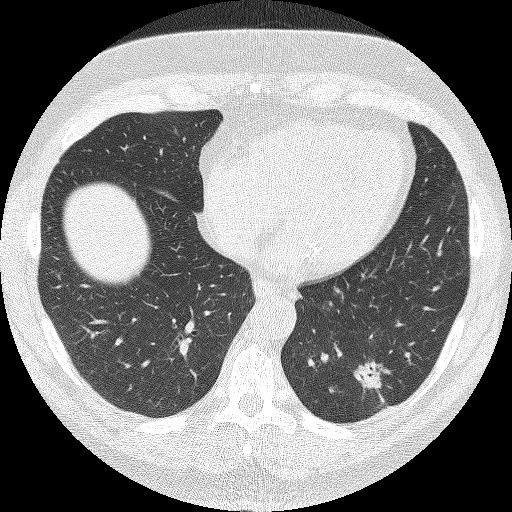
Low-dose screening chest CT, one axial slice; slice 44 of 140 in the series (ordered by position); reconstruction kernel FC51; 120 kVp; lung window (W 1500 / L -600 HU); 512 × 512 image matrix.
Outlined on this slice (expert manual segmentation):
- lesion 1 (tumor, lower lobe of left lung): bounding box [x1, y1, x2, y2] px = [353, 361, 390, 390]